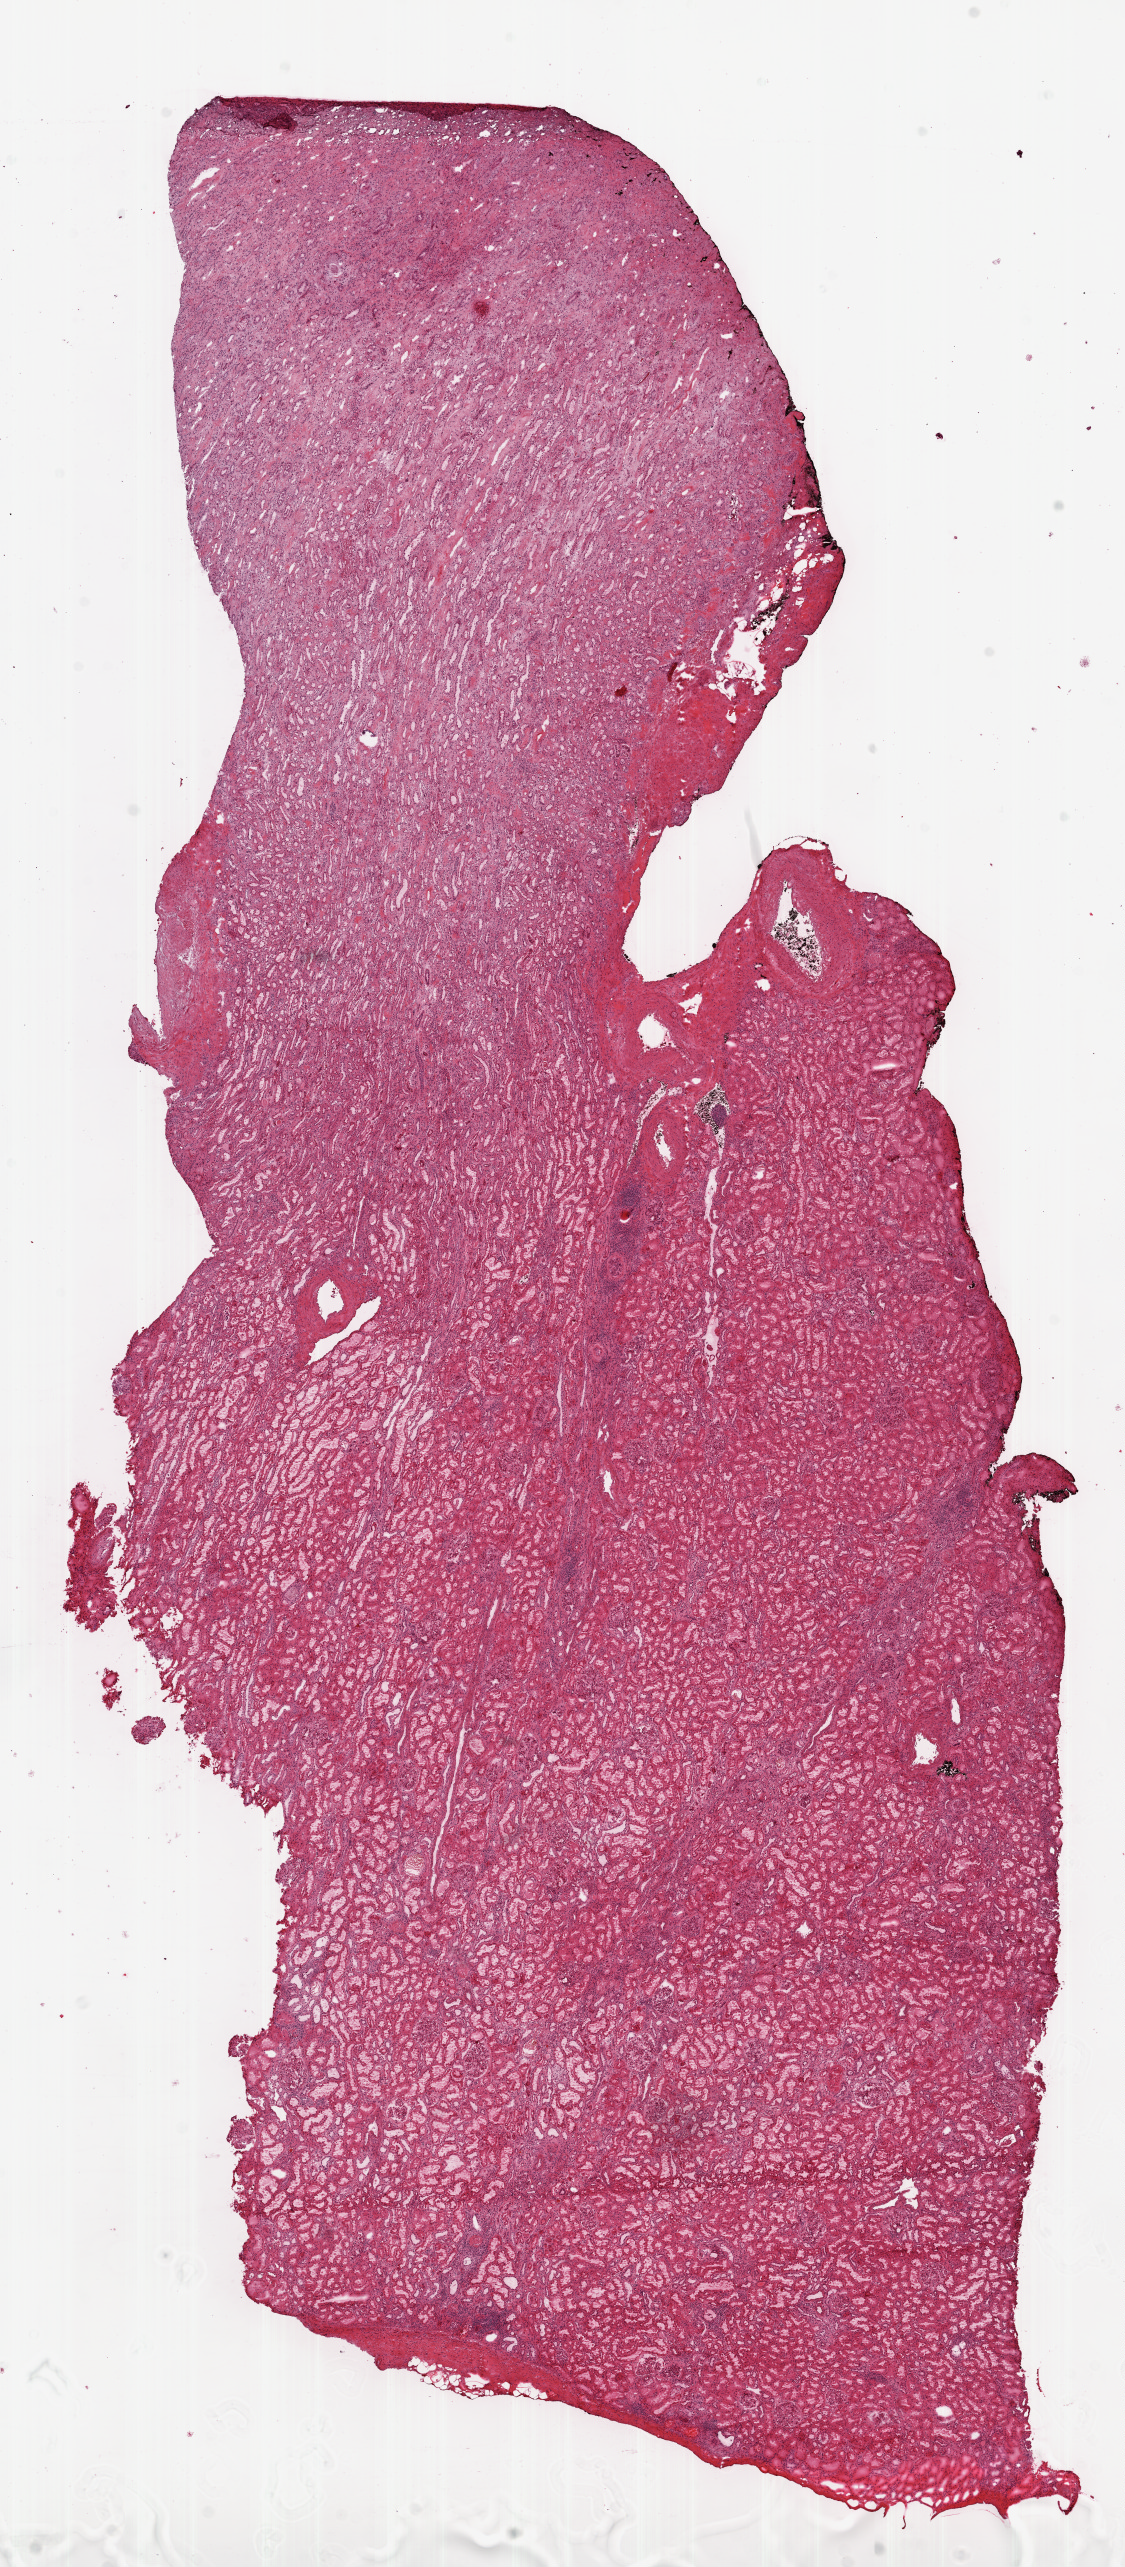
H&E whole-slide image — a low-resolution overview of the entire scanned area, about 9.0 x 20.6 mm (from a 20x scan). Frozen section from the top of the tissue portion. Solid tissue normal (non-tumour tissue) sample from the kidney. Patient: female, age at initial diagnosis 58 years.
* this section: solid tissue normal (non-tumour) sample from the same patient
* patient diagnosis: Clear cell adenocarcinoma, NOS